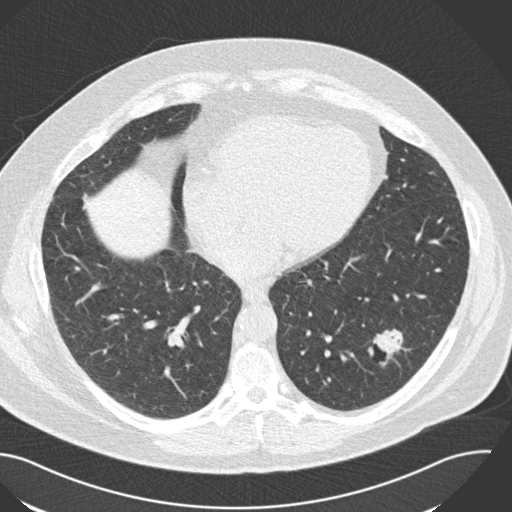
Chest CT (low-dose screening protocol), one axial image. Third annual screen. Lung window (W 1500 / L -600 HU). 2 mm slice thickness. Standard (soft-tissue) reconstruction kernel (B30f). Male, age 57 years at enrolment. Current smoker at enrolment.
• Lesion marked by an expert reader, bounding box [x1, y1, x2, y2] px = [349, 317, 420, 375].
• Screening reader's record for this exam (one nodule recorded; not confirmed to be the boxed lesion): non-calcified nodule or mass ≥4 mm, left lower lobe, 22 × 18 mm, poorly defined margins, soft tissue attenuation, pre-existing on the prior screen: yes; interval growth: yes.
• Official screen result: positive, other.
• Lung cancer was diagnosed 124 days after this screen: squamous cell carcinoma, NOS, left lower lobe, moderately differentiated (G2), stage IA (AJCC 6th edition), 22 mm at pathology.